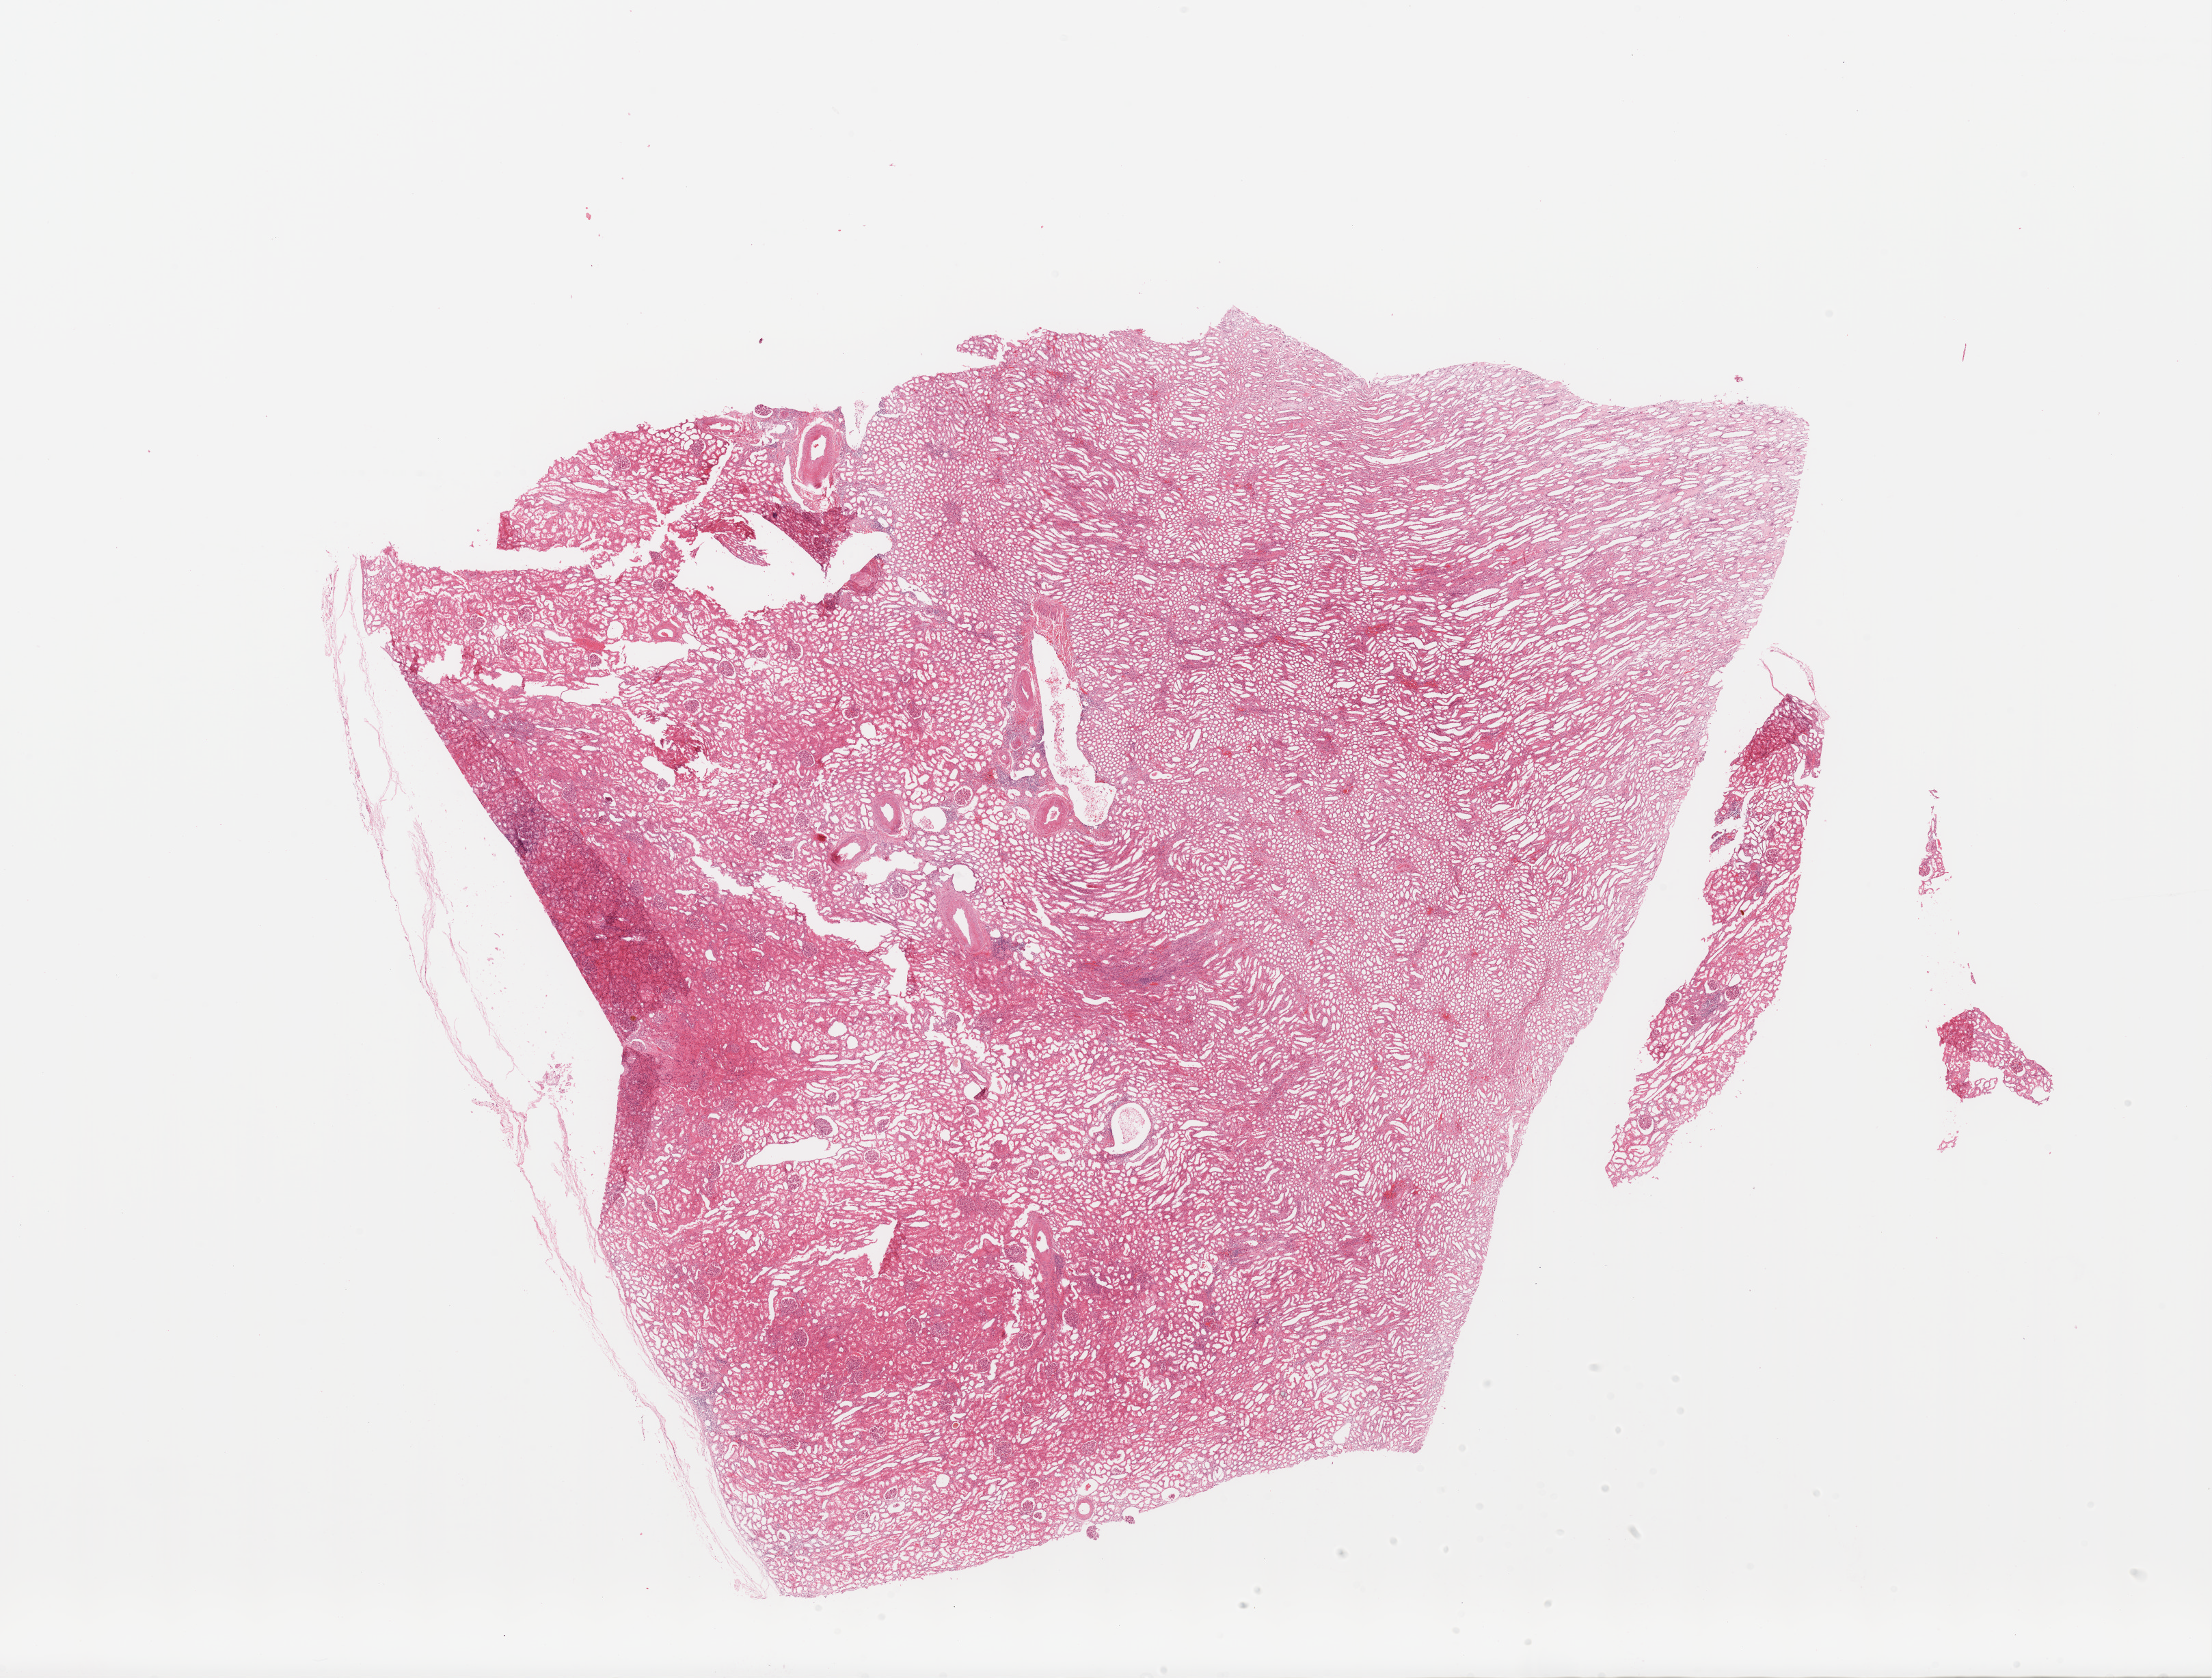
H&E-stained whole-slide image, a low-resolution overview of the entire scanned area, about 25.6 x 19.4 mm (slide scanned at 20x); kidney, normal (non-tumour) tissue. Patient: female, age 52 years.
This section: normal (non-tumour) tissue from the same patient. Patient diagnosis: Renal cell carcinoma, NOS.